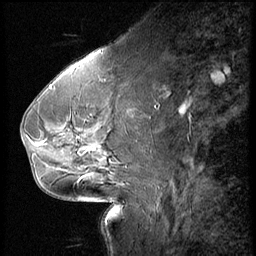
Breast MRI (dynamic contrast-enhanced), one sagittal slice; slice 26 of 66 in the series (ordered by position); 3 images stored at this slice position (order not interpretable as contrast timing); 1.5 T; TE 4.2 ms, TR 8.9 ms; 256 × 256 image matrix, field of view 200 × 200 mm. Patient: female, 54 years. From the clinical record (not read from this slice): setting: breast cancer imaged before/during neoadjuvant chemotherapy; receptor status: HR-positive, HER2-negative.
Annotated regions visible in this slice (semi-automatic segmentation, software-assisted and operator-edited):
- analysis volume of interest (the breast-tissue region the enhancement analysis was run in; not a lesion): box from (x=61, y=104) to (x=146, y=171) px
- tumour enhancement mask (voxels above the 140 % enhancement threshold inside the analysis volume of interest): (x=129, y=110)–(x=132, y=113)